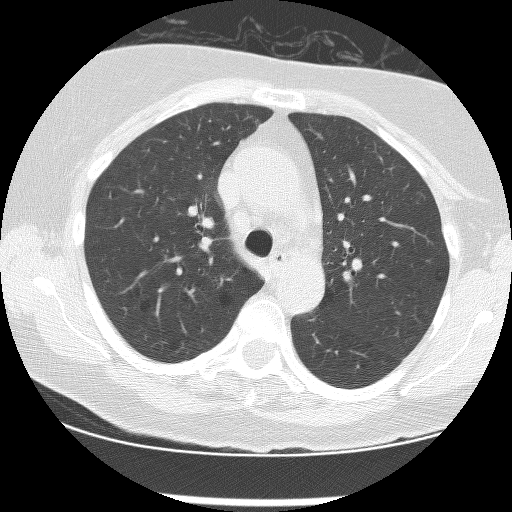
Chest CT (low-dose screening protocol), one axial image; baseline annual screen; lung window (W 1500 / L -600 HU); 2.5 mm slice thickness; lung (sharp) reconstruction kernel (BONE); 120 kVp. Female participant, aged 61 years at enrolment. Current smoker at enrolment.
• Expert-annotated lung lesion, bounding box <243,110,271,138> (left, top, right, bottom; pixels).
• Screening reader's record for this exam: no non-calcified nodule ≥4 mm recorded.
• Official screen result: negative screen, minor abnormalities not suspicious for lung cancer.